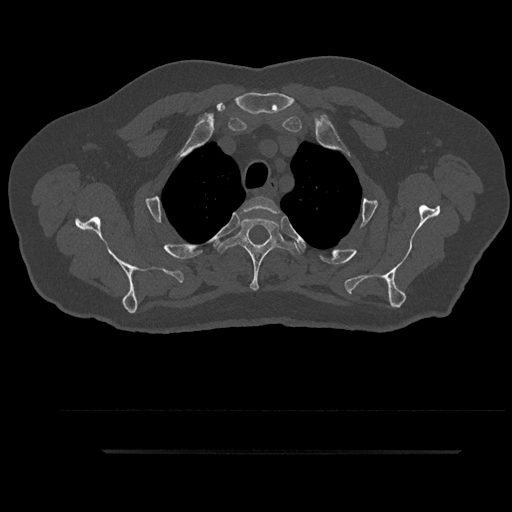
CT including the spine, one axial slice. Slice 723 of 797 in the series (ordered by position). Reconstruction kernel Br40s/3. 120 kVp. Bone window (W 1800 / L 400 HU). 0.5 mm slice thickness. 512 × 512 image matrix, field of view 432 × 432 mm. Male patient, age 63 years. Case-level facts recorded for this patient, not image findings: primary cancer: renal; vertebrae with lytic lesions (as recorded): T8.
Structures marked on this image (semi-automatic segmentation, software-assisted and operator-edited):
- T2 vertebra: bounding box (x1, y1, x2, y2) in pixels: (240, 196, 281, 220)
- T3 vertebra: (217, 217, 300, 291)